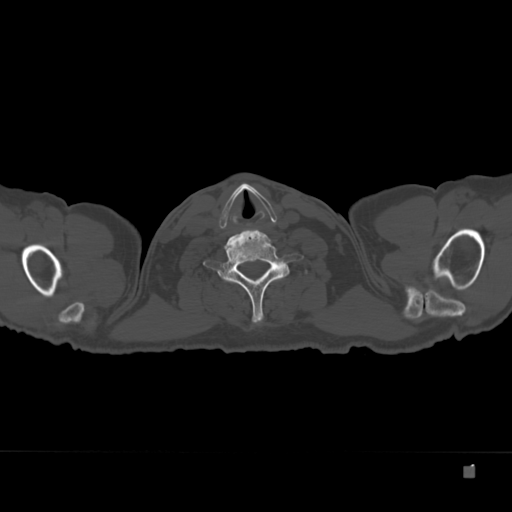
CT including the spine, one axial slice; slice 328 of 332 in the series (ordered by position); reconstruction kernel Br40s; 120 kVp; bone window (W 1800 / L 400 HU); 512 × 512 image matrix, field of view 389 × 389 mm. Patient: male, 72 years. From the clinical record (not read from this slice): primary cancer: skeletal.
Outlined on this slice (semi-automatically segmented with operator editing):
- T1 vertebra: box from (x=245, y=270) to (x=307, y=281) px